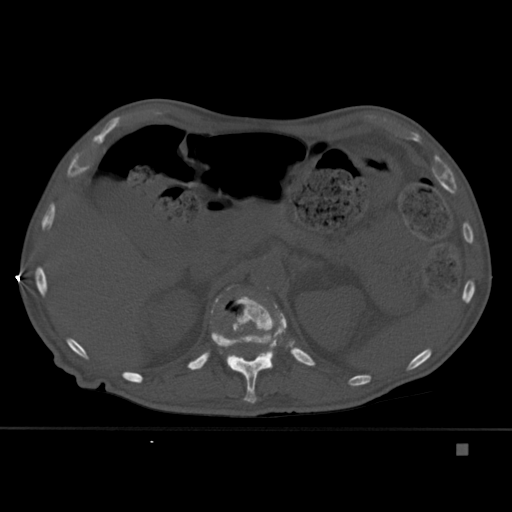
CT including the spine, one axial slice; bone window (W 1800 / L 400 HU); 1.5 mm slice thickness; 512 × 512 image matrix. Patient: male, 75 years. From the clinical record (not read from this slice): primary cancer: prostate.
Annotated regions visible in this slice (semi-automatically segmented with operator editing):
- L1 vertebra: bounding box [x1, y1, x2, y2] px = [212, 286, 268, 362]
- T12 vertebra: [210, 295, 287, 404]